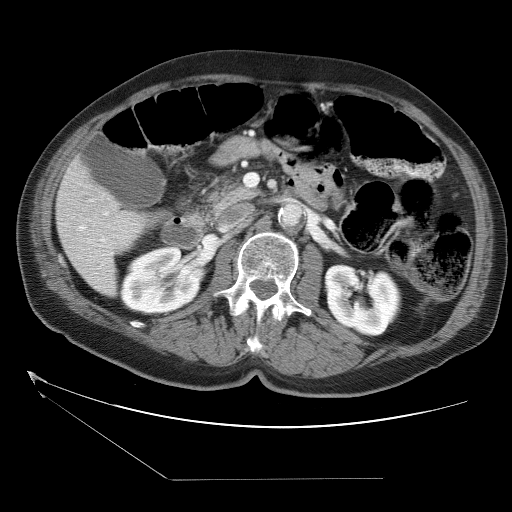
Contrast-enhanced abdominal CT (liver protocol), one axial slice; position 11 of 38 along the scan axis; one of 2 acquisitions stored at this slice position; soft-tissue window (W 400 / L 40 HU); 512 × 512 image matrix. Case-level facts recorded for this patient, not image findings: diagnosis: hepatocellular carcinoma (patient treated with transarterial chemoembolisation; whether this scan precedes or follows treatment is not stated here); TNM stage (as recorded): Stage-II; Child-Pugh class: A; tumour differentiation: moderately differentiated; tumour nodularity: multinodular.
Structures marked on this image (semi-automatically segmented with operator editing):
- liver parenchyma outside the tumour (the mass and vessels are separate outlines, so this box may not span the whole liver): bounding box (x1, y1, x2, y2) in pixels: (56, 156, 146, 294)
- liver vessels: (78, 226, 107, 260)